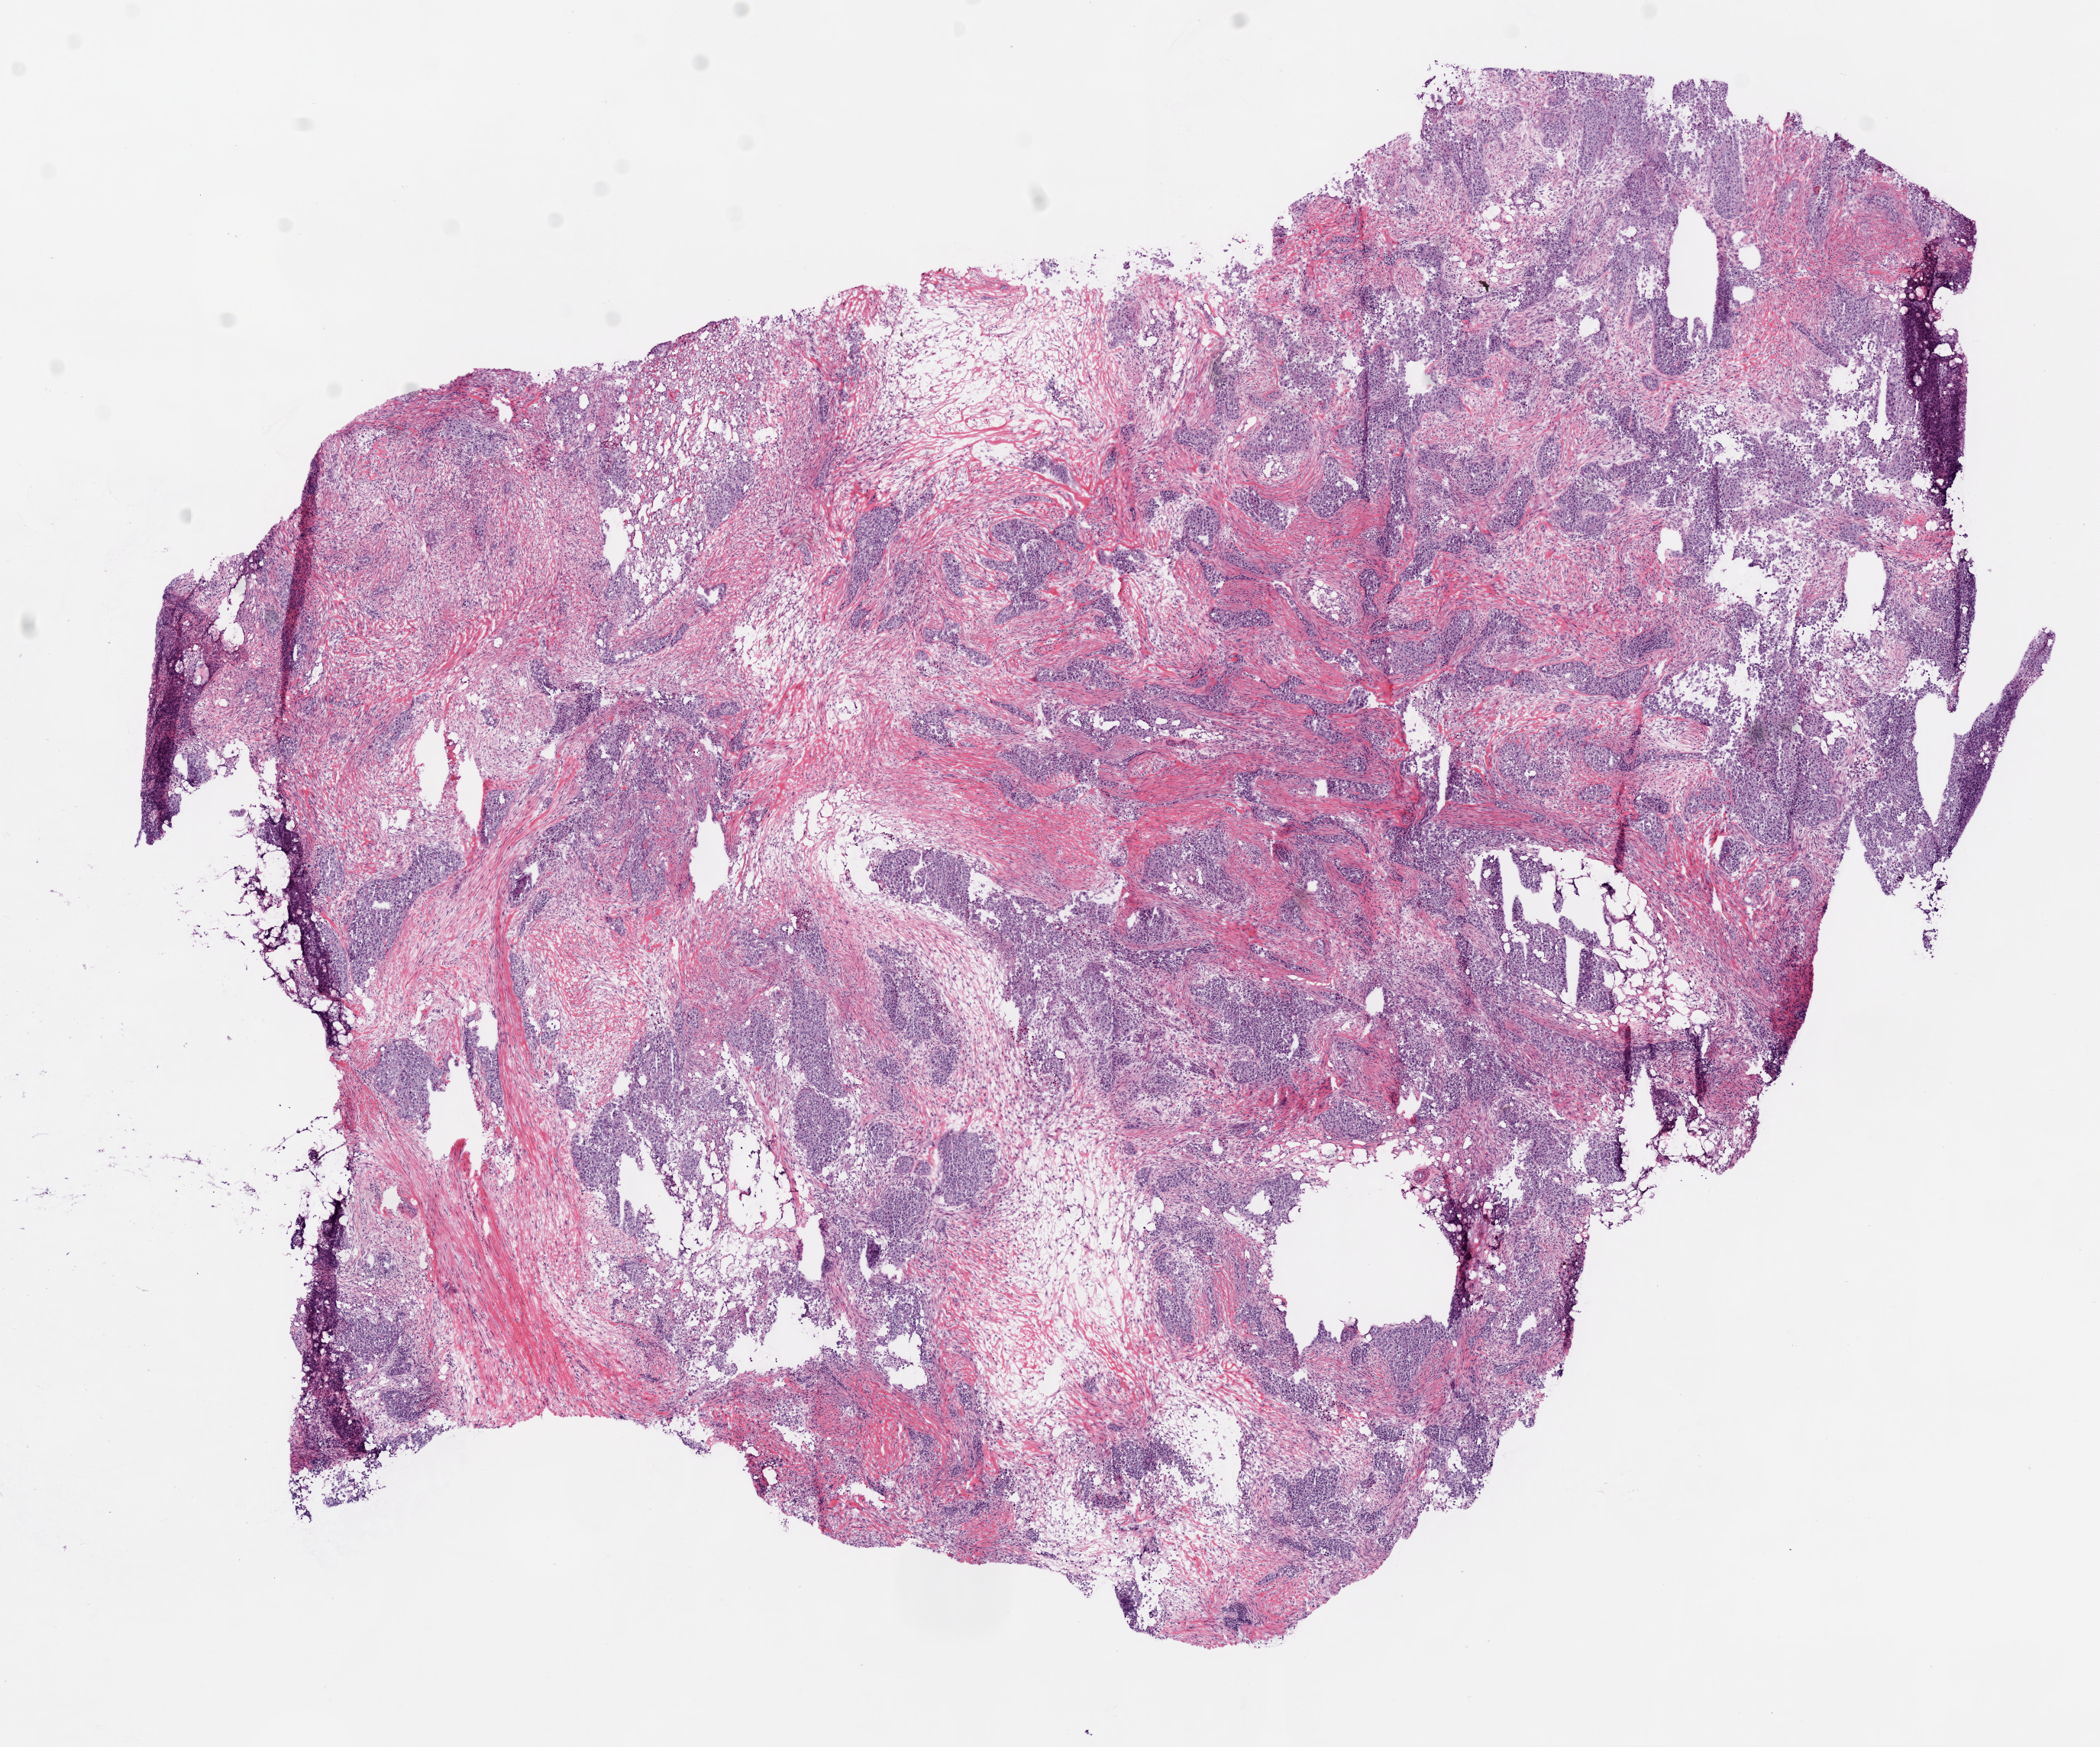
H&E whole-slide image — shown as a low-resolution overview of the whole scanned area (about 11.0 x 9.2 mm), frozen section from the bottom of the tissue portion, ovary, primary tumour sample. Patient: female, age at initial diagnosis 75 years.
Histologic diagnosis: Serous cystadenocarcinoma, NOS.